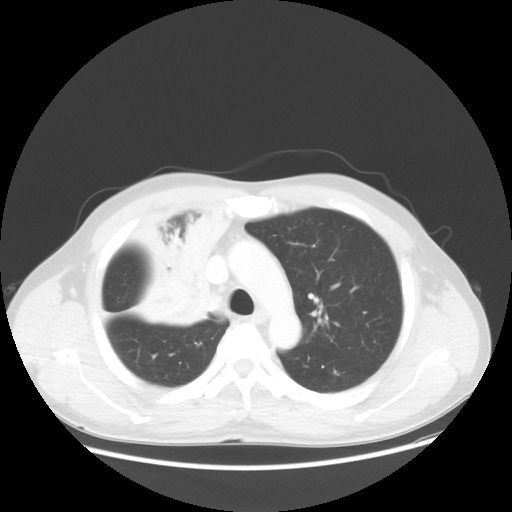
Chest CT, one axial slice; position 39 of 56 along the scan axis; reconstruction kernel STANDARD; lung window (W 1500 / L -600 HU); 5 mm slice thickness; 512 × 512 image matrix. Patient: male, 60 years. Case-level facts recorded for this patient, not image findings: clinical TNM (as recorded): T2a N1 M0.
Annotated regions visible in this slice (bounding box drawn by a radiologist):
- lung tumour (recorded histology: squamous cell carcinoma): bounding box <131,186,248,333> (left, top, right, bottom; pixels)